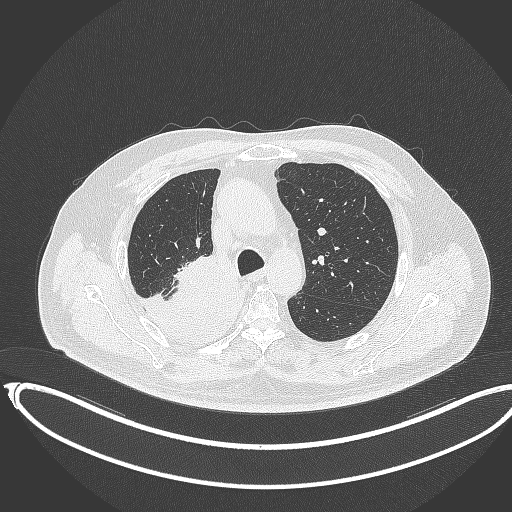
Chest CT, one axial slice; reconstruction kernel B70f; 120 kVp; lung window (W 1500 / L -600 HU); 1 mm slice thickness; 512 × 512 image matrix. Male patient, age 68 years. Case-level facts recorded for this patient, not image findings: clinical TNM (as recorded): T2a N0 M0.
Structures marked on this image (rectangle marked by the reading radiologist):
- lung tumour (recorded histology: adenocarcinoma): box from (x=130, y=255) to (x=250, y=352) px